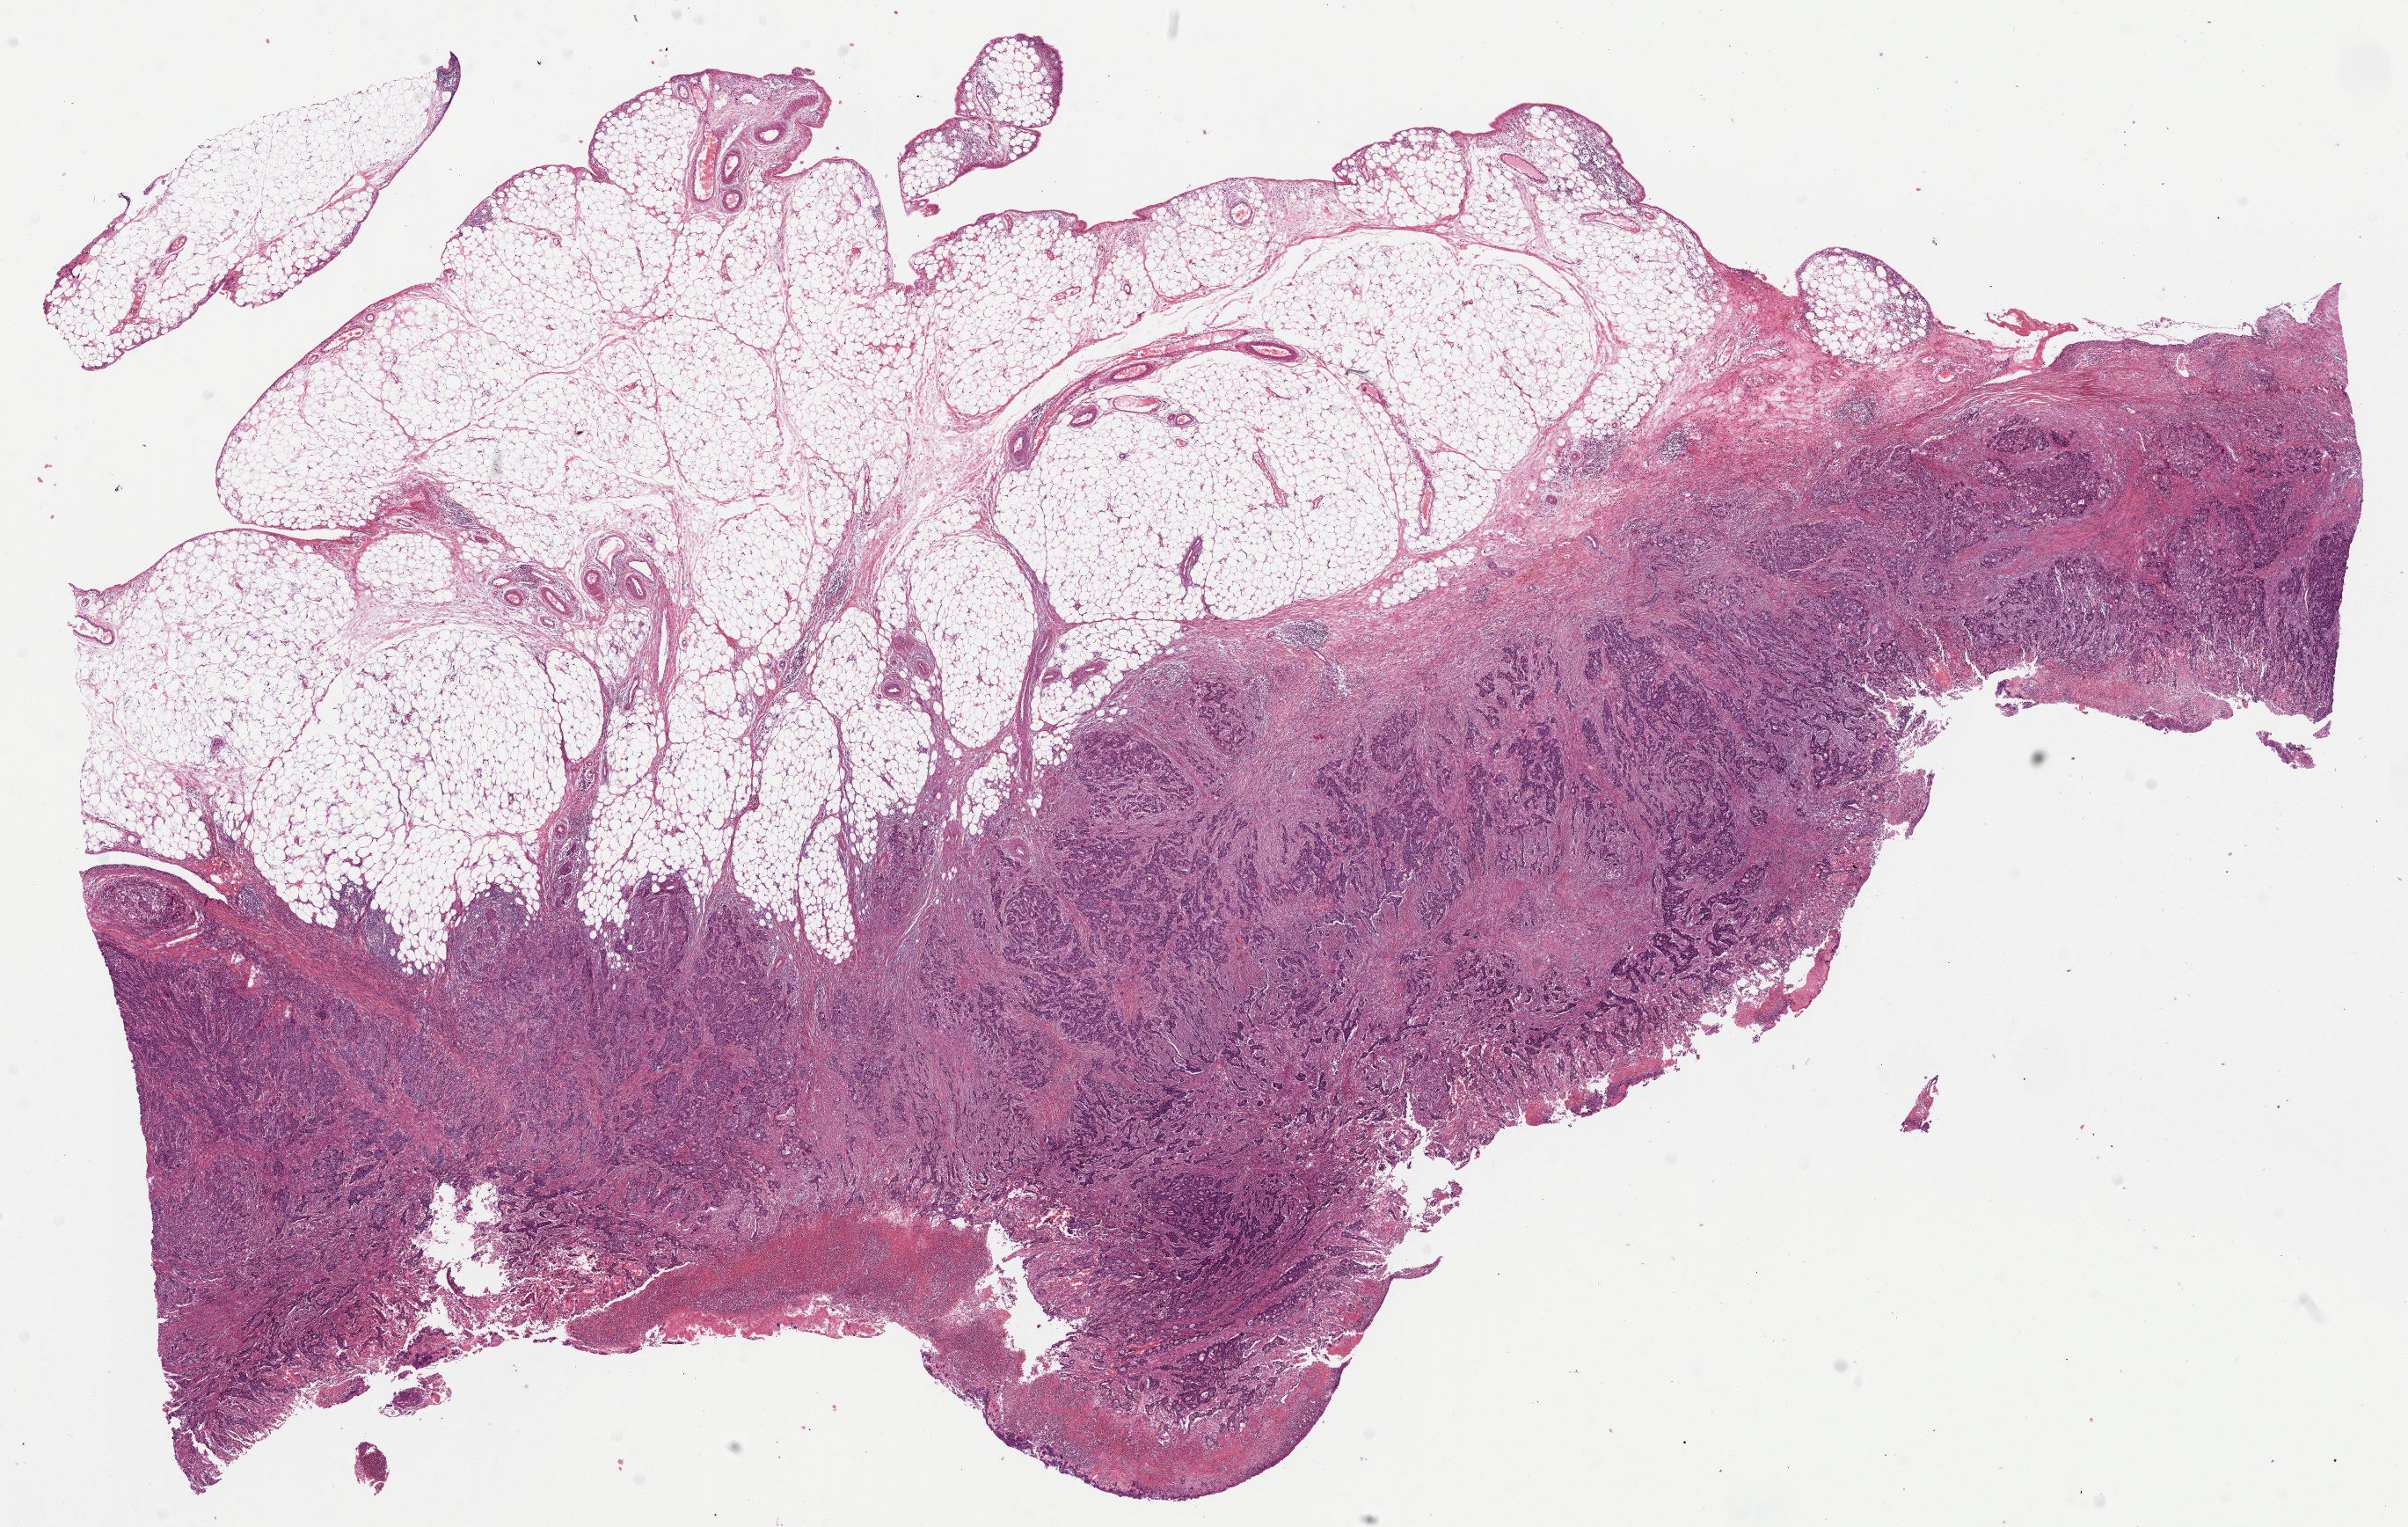
H&E whole-slide image — whole scanned area (about 21.7 x 13.7 mm) shown as a low-resolution overview, FFPE section, sample: primary tumour, stomach. Patient: female, age at initial diagnosis 71 years. Histologic grade: G3 (poorly differentiated).
Lymph nodes positive (case pathology): 1 of 64 examined. Histologic diagnosis: Carcinoma, diffuse type (gastric antrum). AJCC pathologic stage: IIB (7th edition).